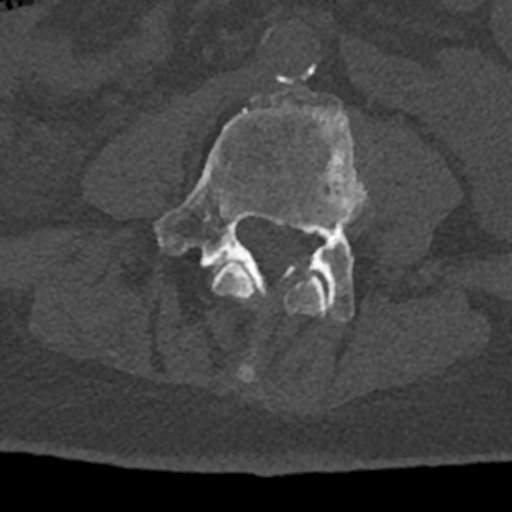
CT including the spine, one axial slice; slice 274 of 797 in the series (ordered by position); 120 kVp; bone window (W 1800 / L 400 HU); 0.5 mm slice thickness; 512 × 512 image matrix. Male patient, age 74 years. Case-level facts recorded for this patient, not image findings: primary cancer: renal.
Structures marked on this image (semi-automatically segmented with operator editing):
- L3 vertebra: bounding box <211,261,327,381> (left, top, right, bottom; pixels)
- L4 vertebra: <155,86,367,321>